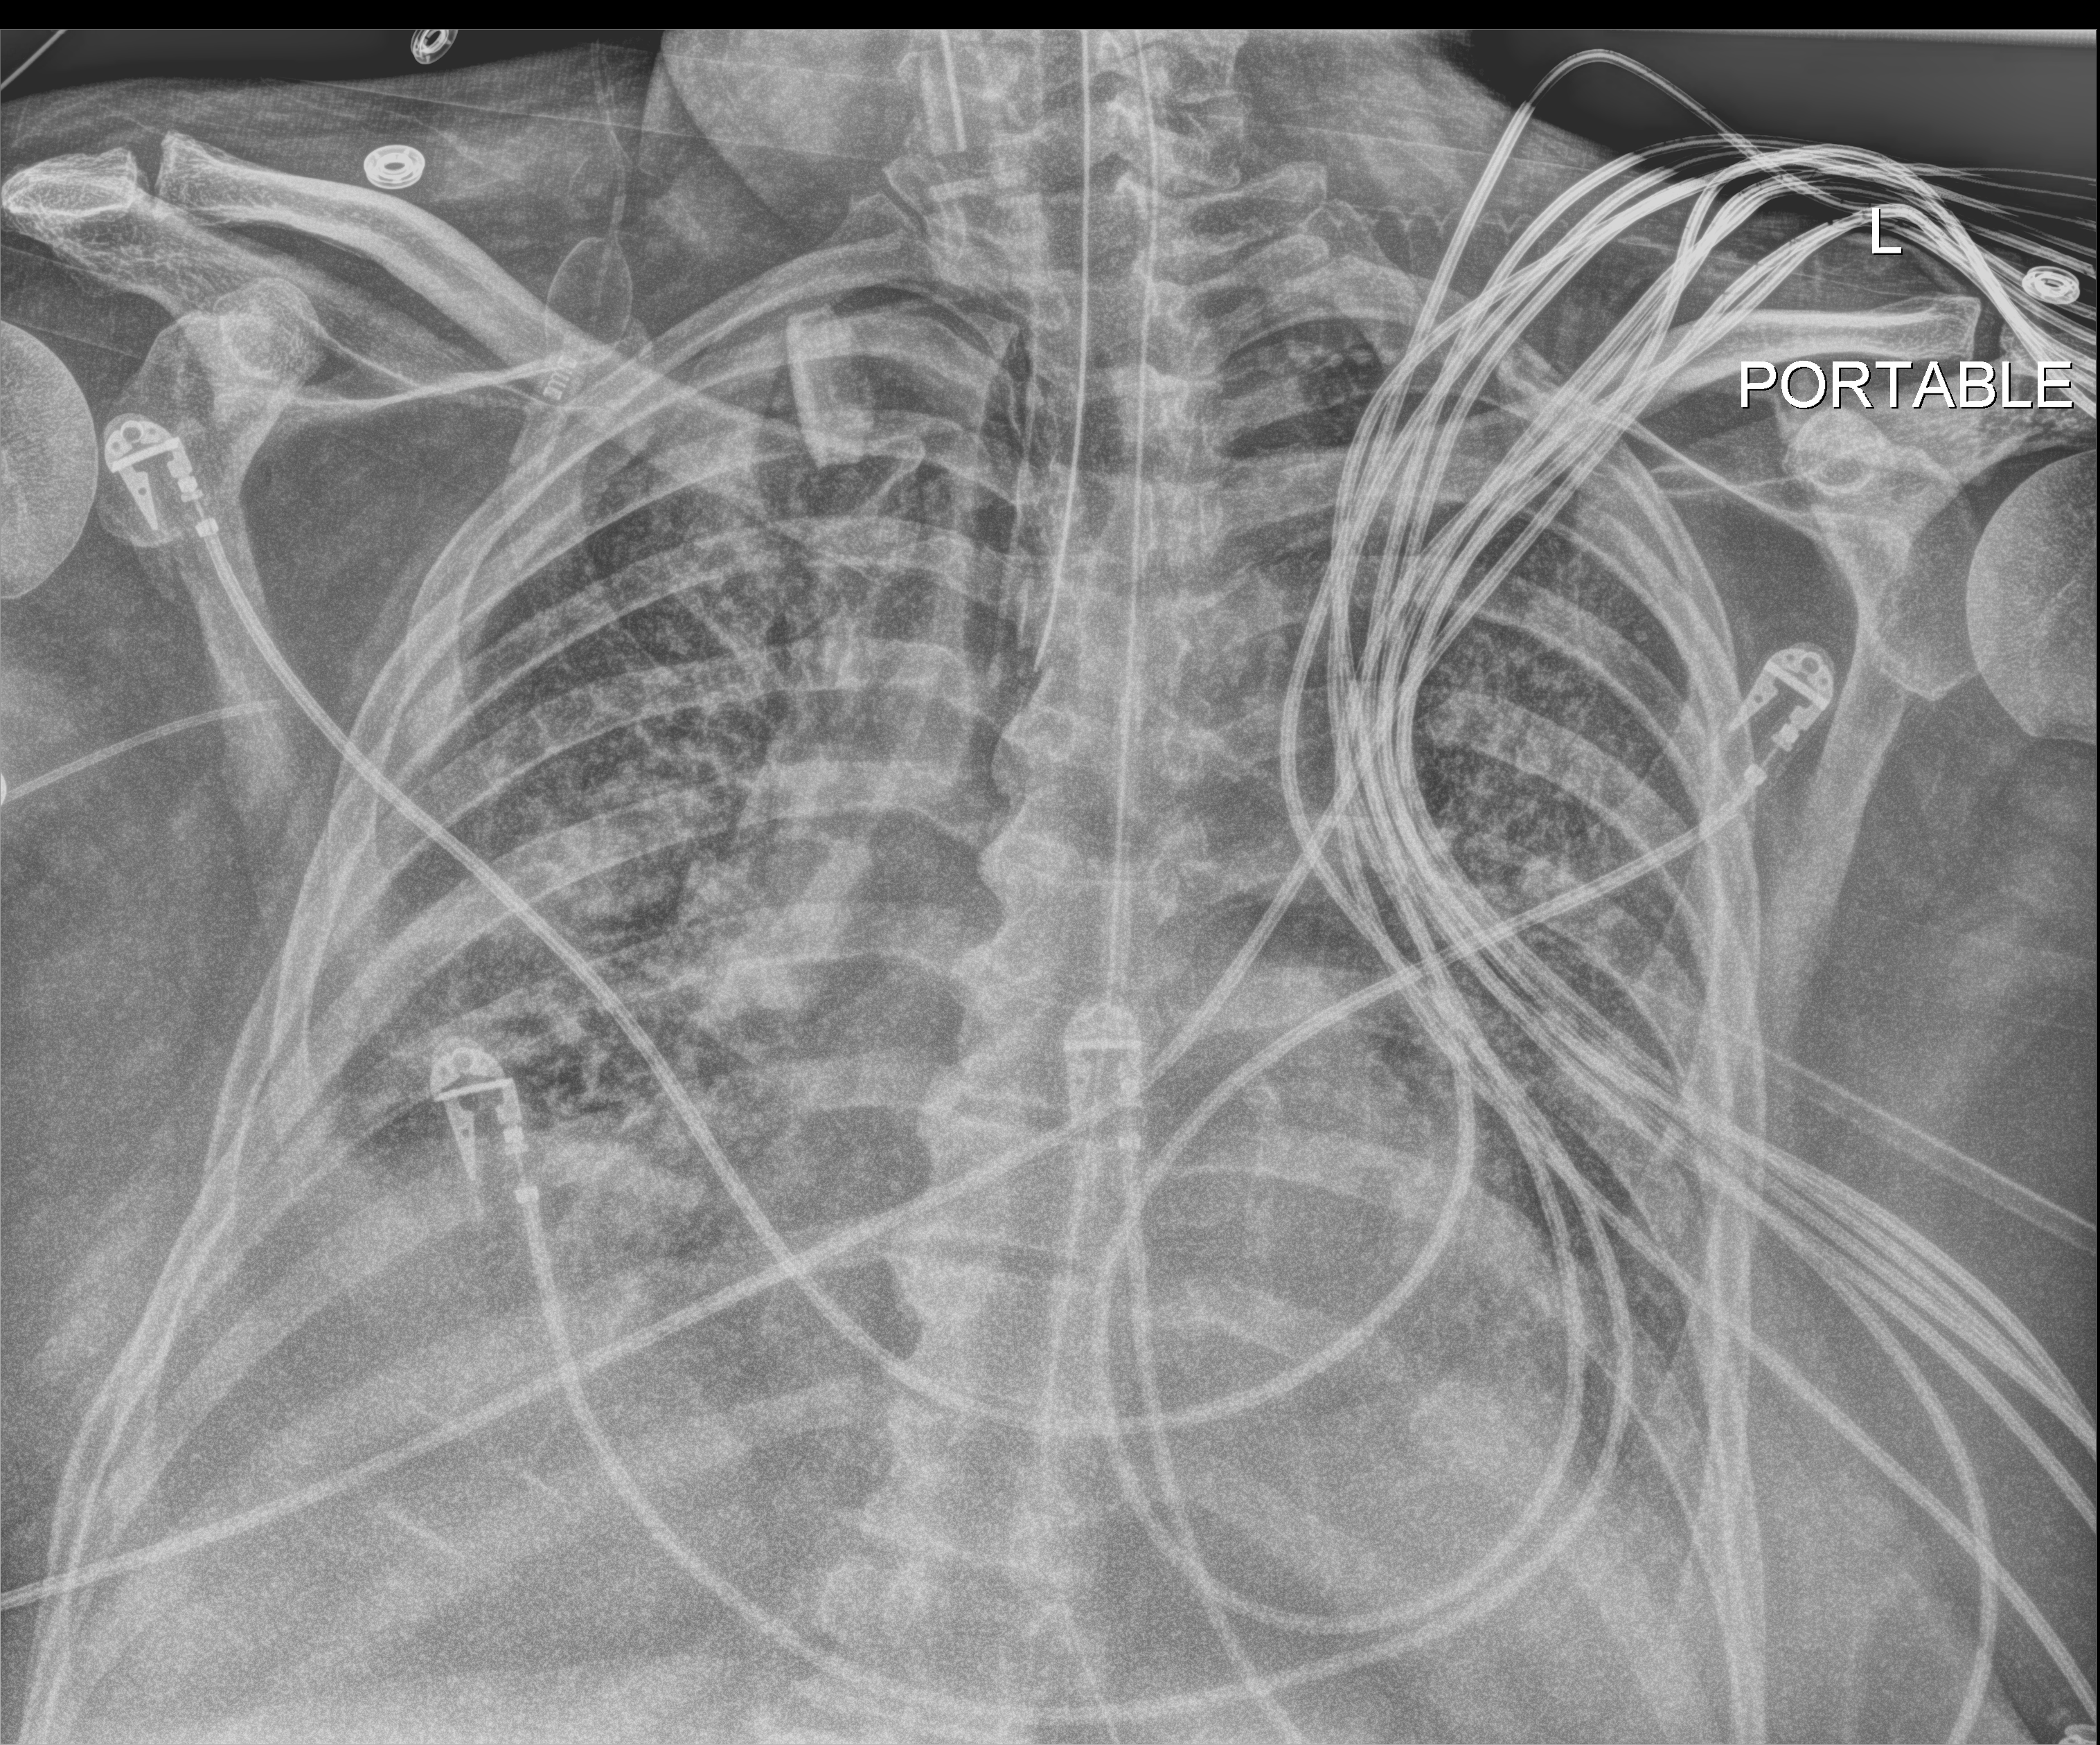
Portable chest radiograph. Patient hospitalised with COVID-19; male, aged 60–74 years.
Hospital-stay facts (about this admission, not read from this image; timing relative to this image not recorded):
- mechanically ventilated during this hospital stay: yes
- COPD (admission record): no